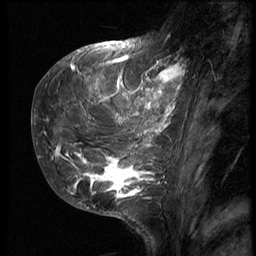
Breast MRI (dynamic contrast-enhanced), one sagittal slice. Slice 18 of 62 in the series (ordered by position). 3 images stored at this slice position (order not interpretable as contrast timing). 1.5 T. TE 4.2 ms, TR 9 ms. 256 × 256 image matrix, field of view 180 × 180 mm. Female patient, age 28 years. From the clinical record (not read from this slice): setting: breast cancer imaged before/during neoadjuvant chemotherapy.
Outlined on this slice (semi-automatic segmentation, software-assisted and operator-edited):
- analysis volume of interest (the breast-tissue region the enhancement analysis was run in; not a lesion): bounding box <42,48,192,207> (left, top, right, bottom; pixels)
- tumour enhancement mask (voxels above the 140 % enhancement threshold inside the analysis volume of interest): <46,54,185,203>